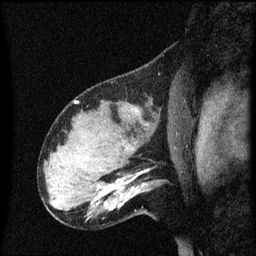
Breast MRI (dynamic contrast-enhanced), one sagittal slice. Position 43 of 60 along the scan axis. Dynamic contrast-enhanced series, image 2 of 3 at this slice position (ordered by acquisition). 1.5 T. TE 4.2 ms, TR 8.4 ms. 256 × 256 image matrix, field of view 200 × 200 mm. Female patient, age 31 years. Case-level facts recorded for this patient, not image findings: setting: breast cancer imaged before/during neoadjuvant chemotherapy; receptor status: HR-positive, HER2-negative.
Structures marked on this image (semi-automatically segmented with operator editing):
- analysis volume of interest (the breast-tissue region the enhancement analysis was run in; not a lesion): box from (x=102, y=166) to (x=161, y=219) px
- tumour enhancement mask (voxels above the 70 % enhancement threshold inside the analysis volume of interest): (x=107, y=180)–(x=130, y=193)